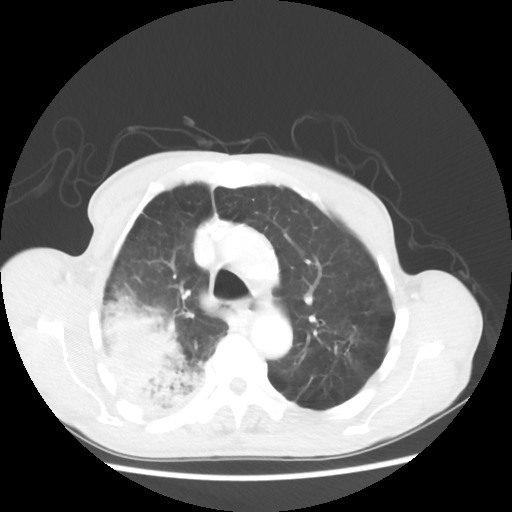
Chest CT, one axial slice; position 40 of 58 along the scan axis; 100 kVp; lung window (W 1500 / L -600 HU); 5 mm slice thickness; 512 × 512 image matrix, field of view 351 × 351 mm. Male patient, age 75 years. Case-level facts recorded for this patient, not image findings: clinical TNM (as recorded): T4 N1 M1.
Structures marked on this image (bounding box drawn by a radiologist):
- lung tumour (recorded histology: adenocarcinoma): bounding box <93,283,208,414> (left, top, right, bottom; pixels)